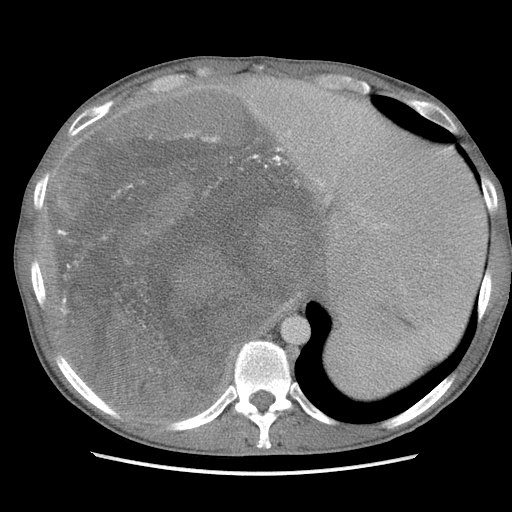
Contrast-enhanced abdominal CT, one axial slice; slice 85 of 115 in the series (ordered by position); soft-tissue window (W 400 / L 40 HU); 5 mm slice thickness; 512 × 512 image matrix, field of view 360 × 360 mm. Male patient. Case-level facts recorded for this patient, not image findings: diagnosis: adrenocortical carcinoma; tumour side: right adrenal; Ki-67 index: 13 %; stage (as recorded): 3.
Annotated regions visible in this slice (semi-automatically segmented with operator editing):
- mass: bounding box <55,91,319,417> (left, top, right, bottom; pixels)